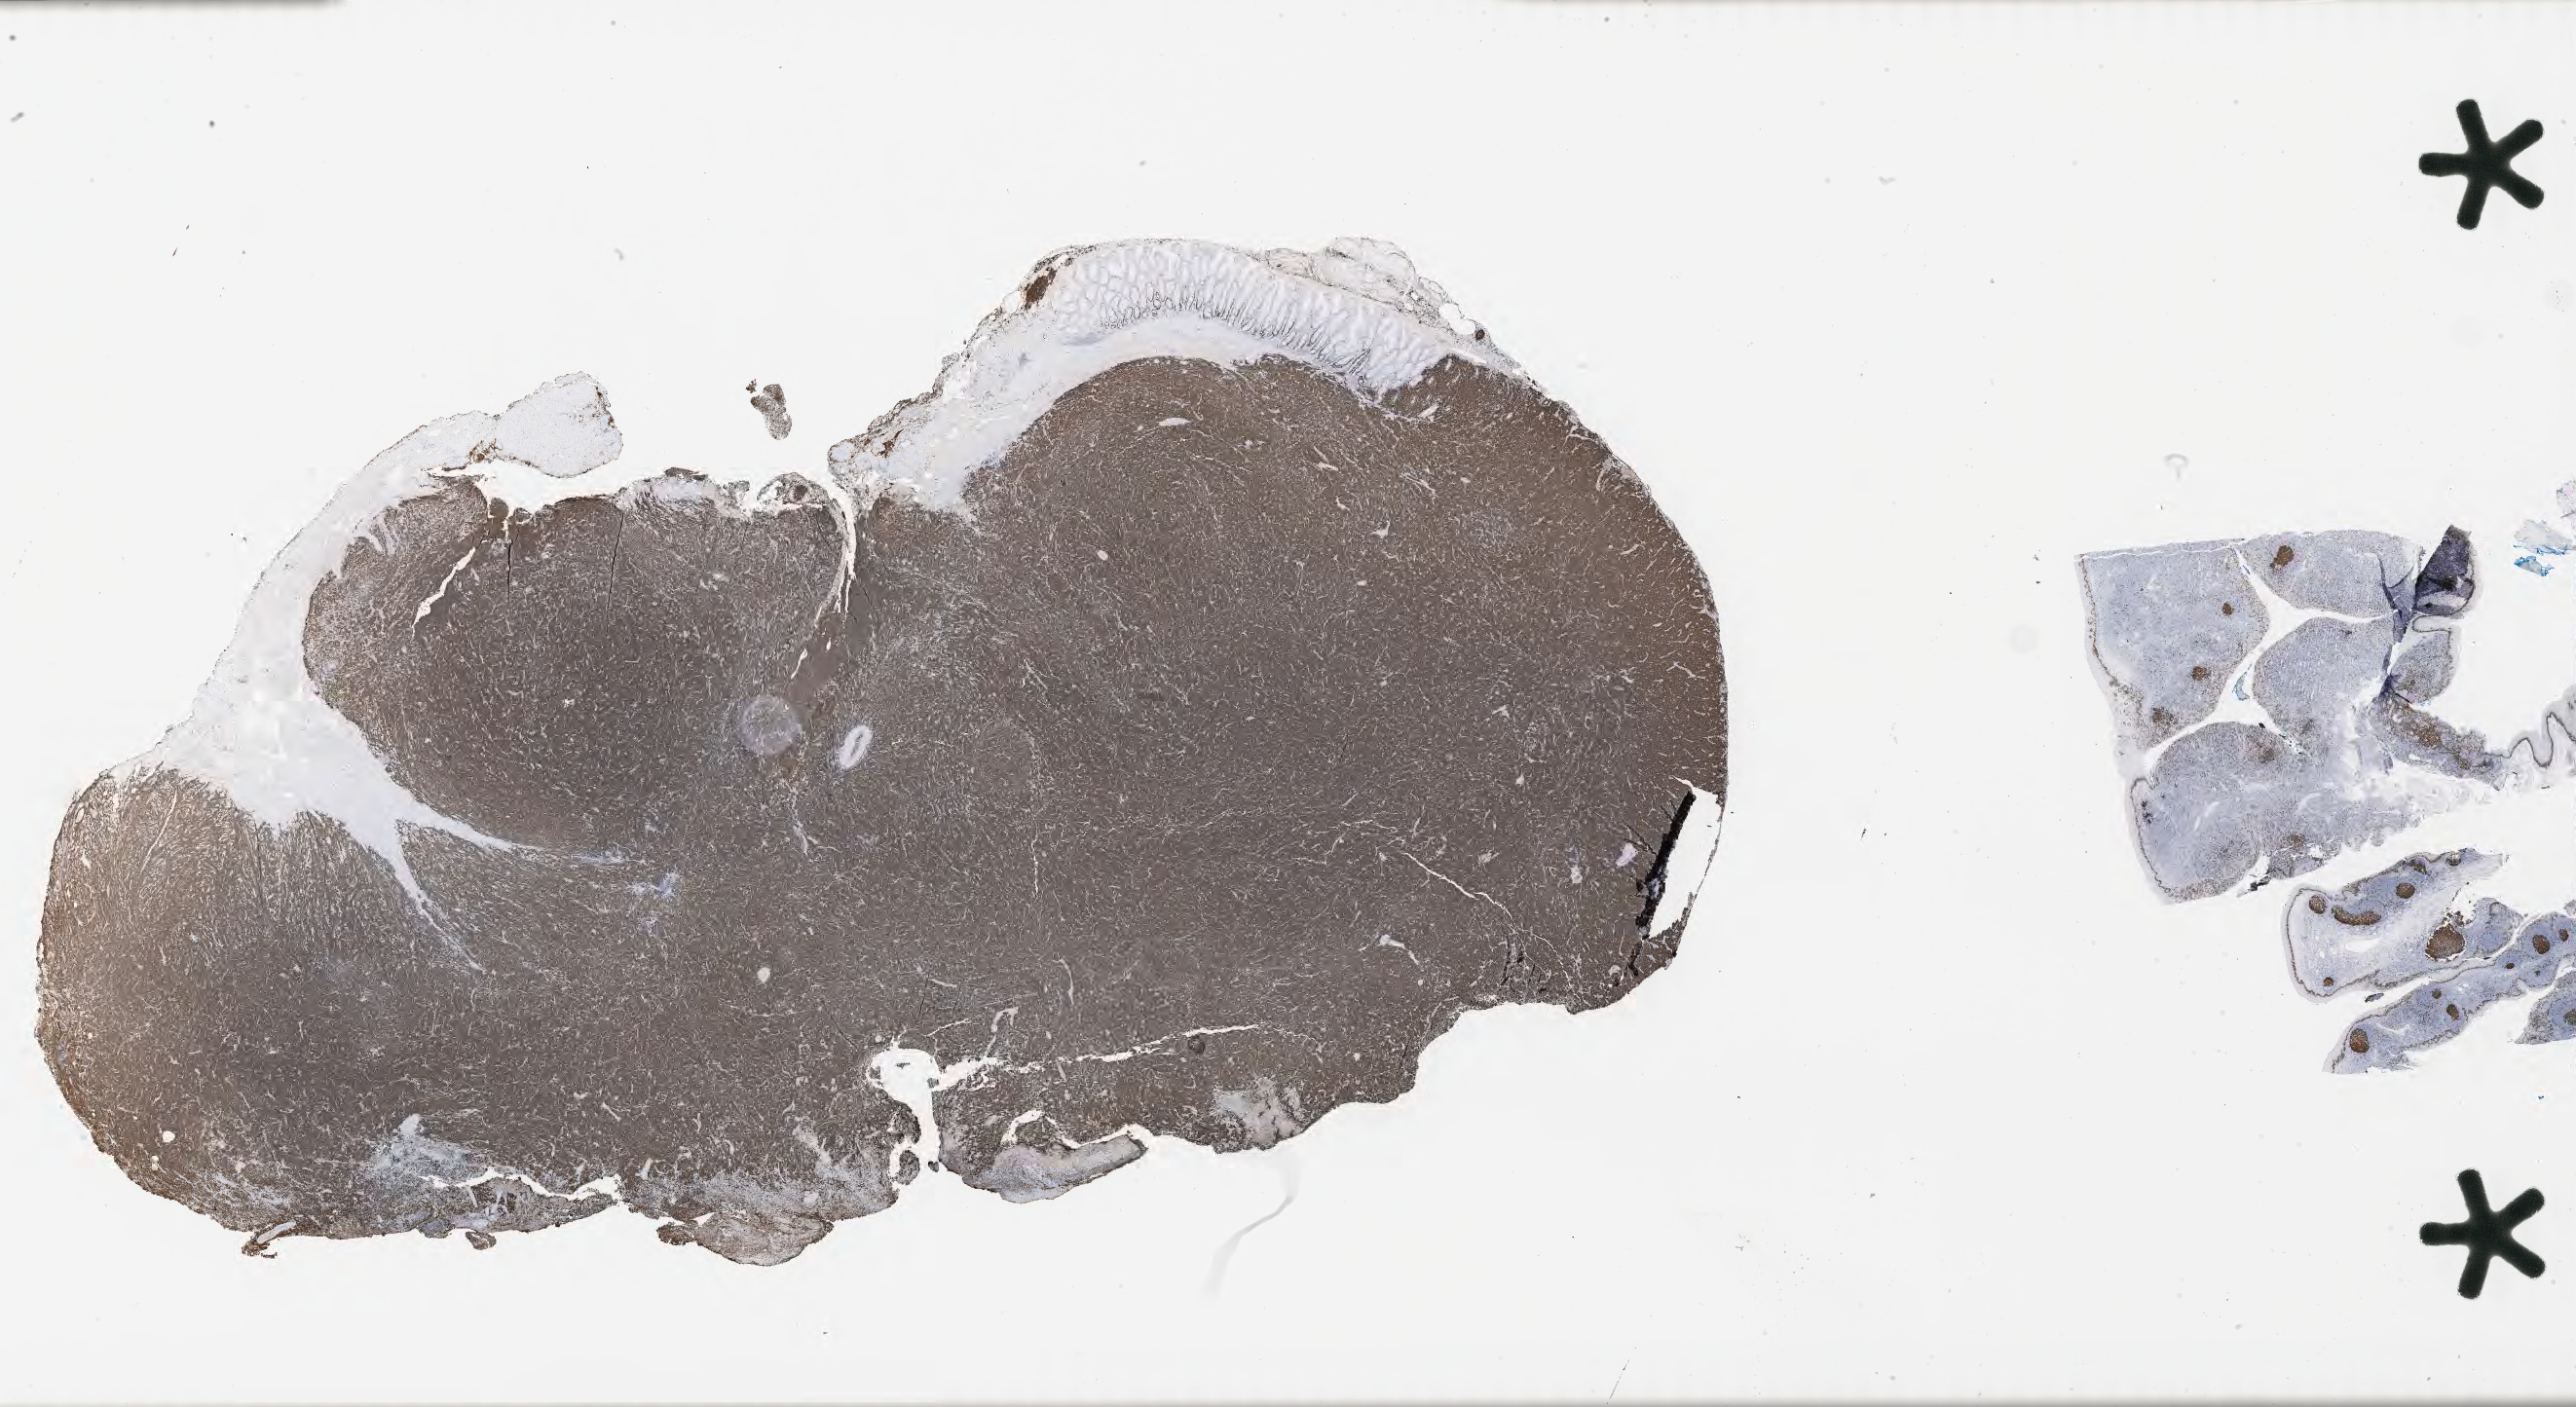
Immunohistochemistry (IHC) whole-slide image stained for Ki-67, shown as a low-resolution overview of the whole scanned area (about 42.8 x 23.4 mm). Specimen: tumor tissue. Patient female; age 29 years.
* histologic diagnosis: Burkitt lymphoma, NOS